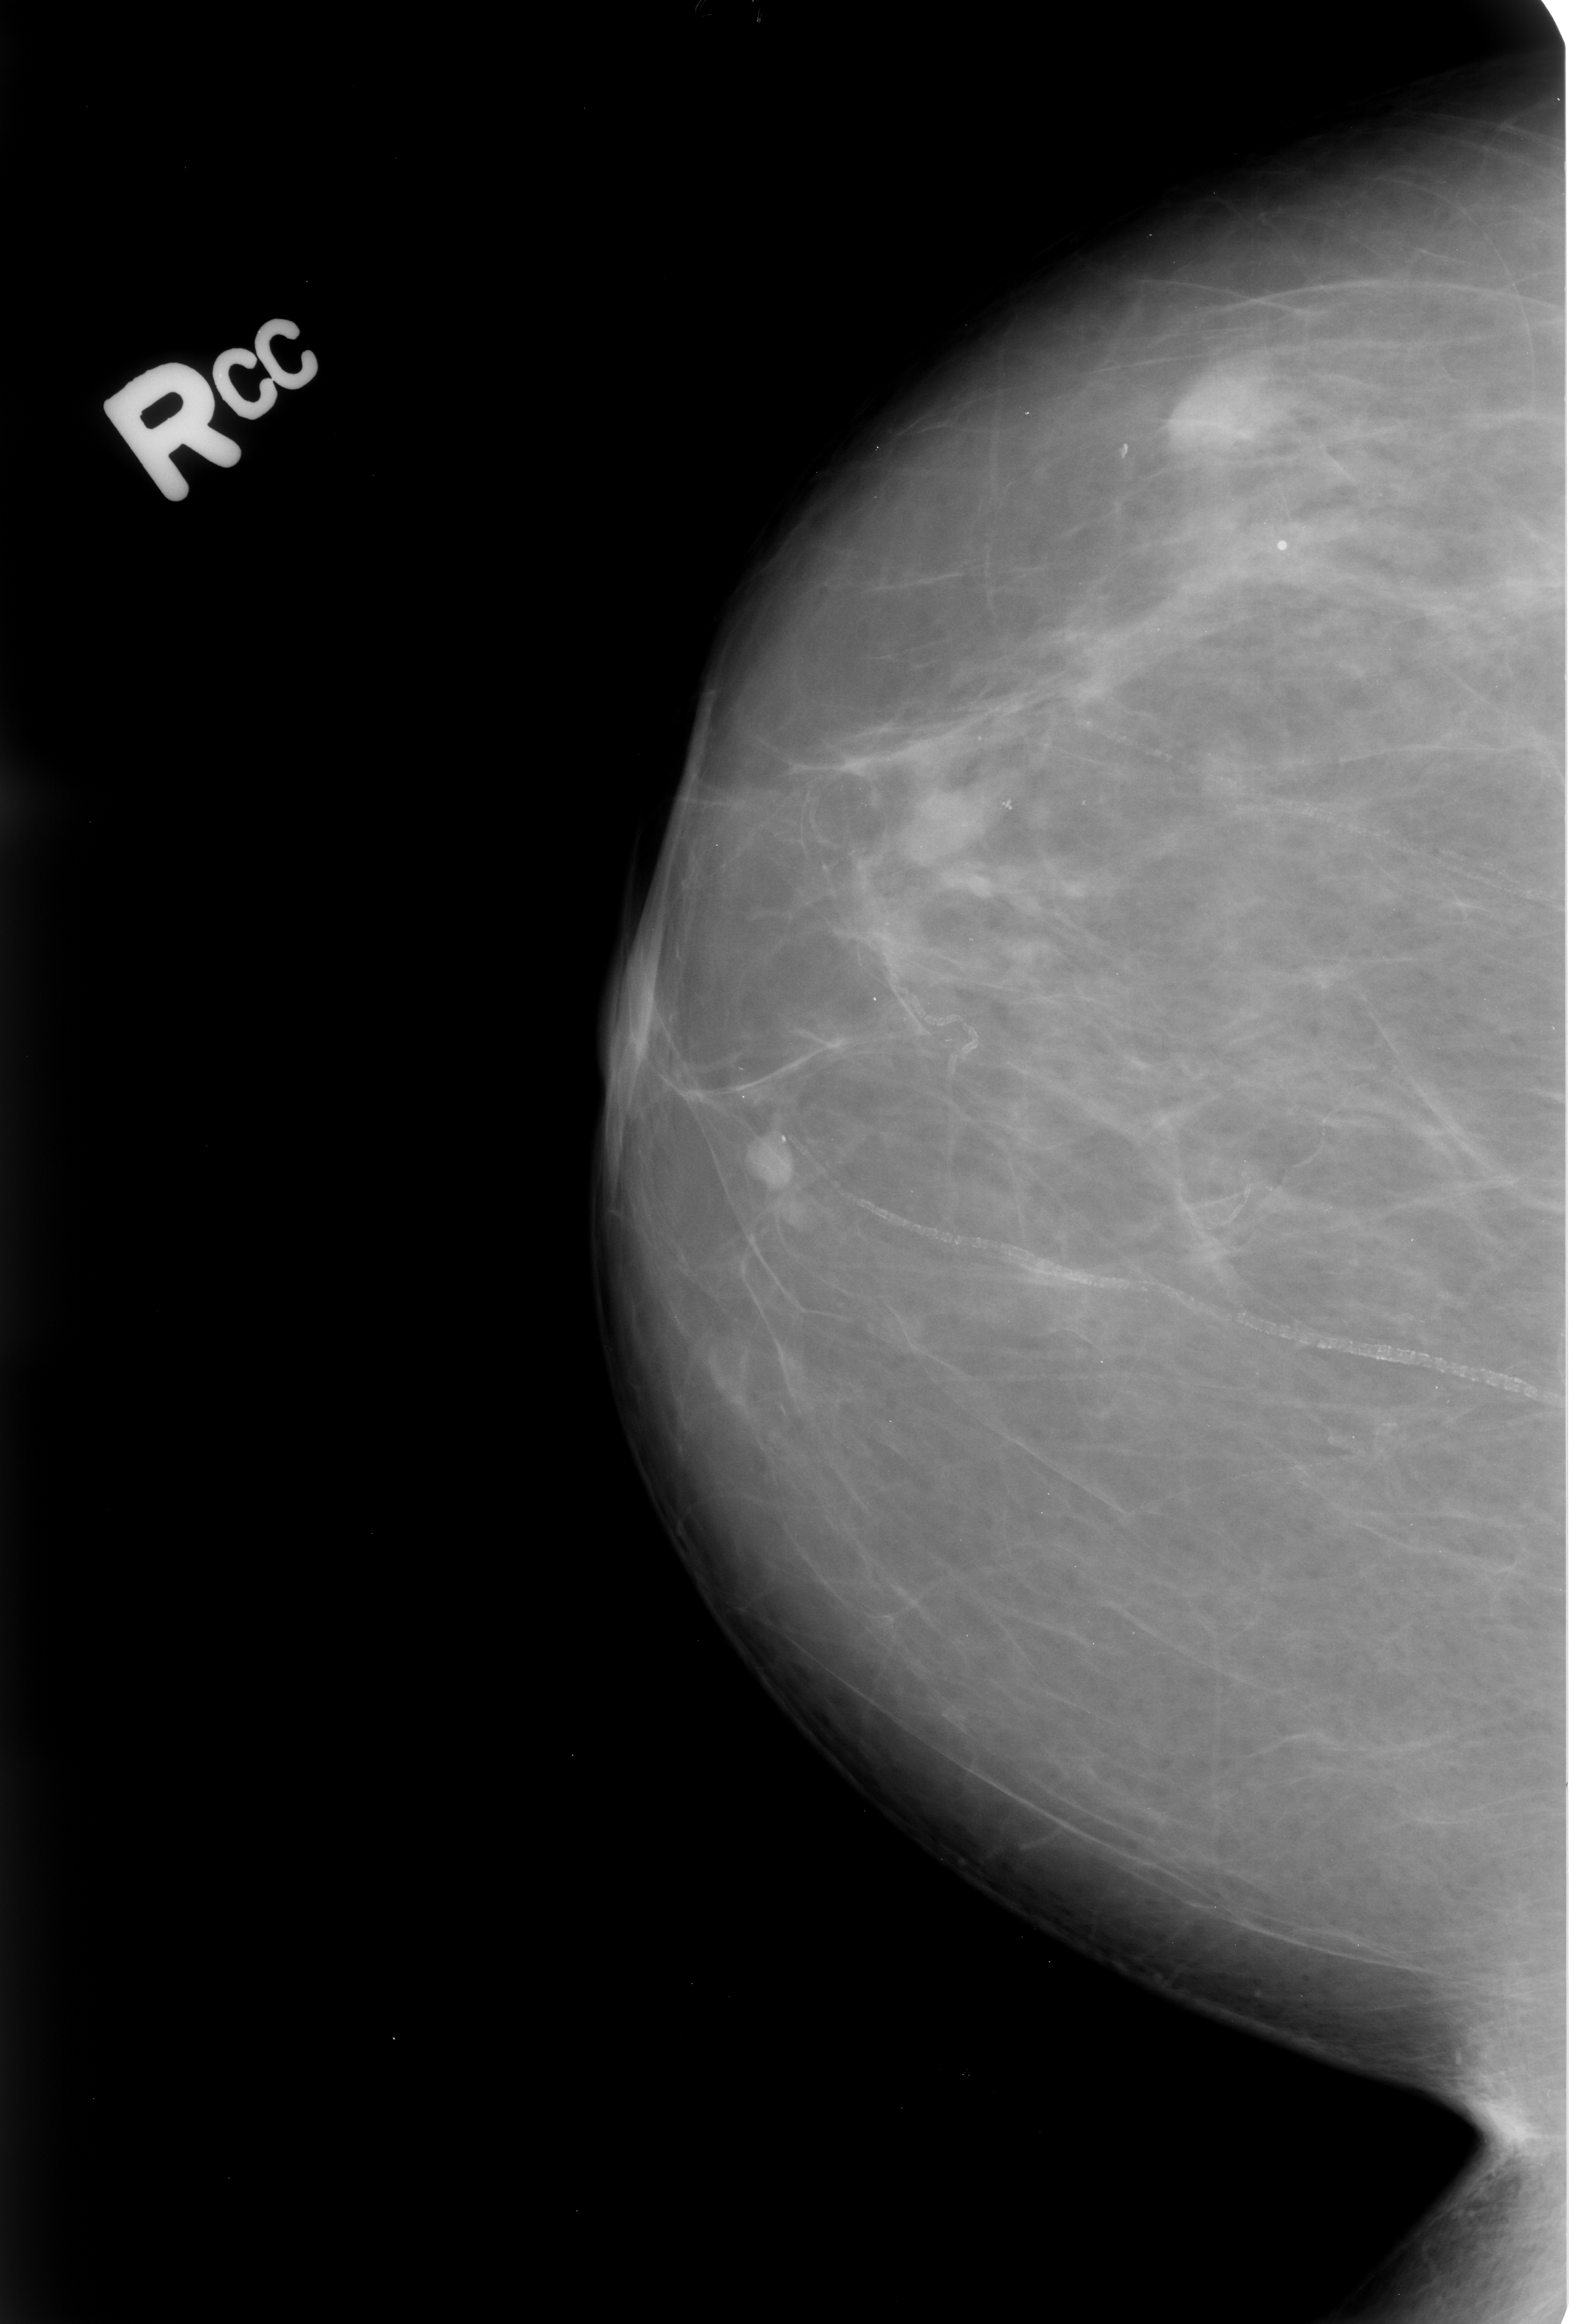
Mammogram (digitized film); right breast; craniocaudal (CC) view; breast composition: scattered fibroglandular densities (BI-RADS density category 2 of 4).
Marked findings (only marked abnormalities are described; nothing is implied about the rest of the image): mass, shape asymmetric breast tissue; BI-RADS assessment category 2; benign; no additional work-up was recommended (benign without callback).